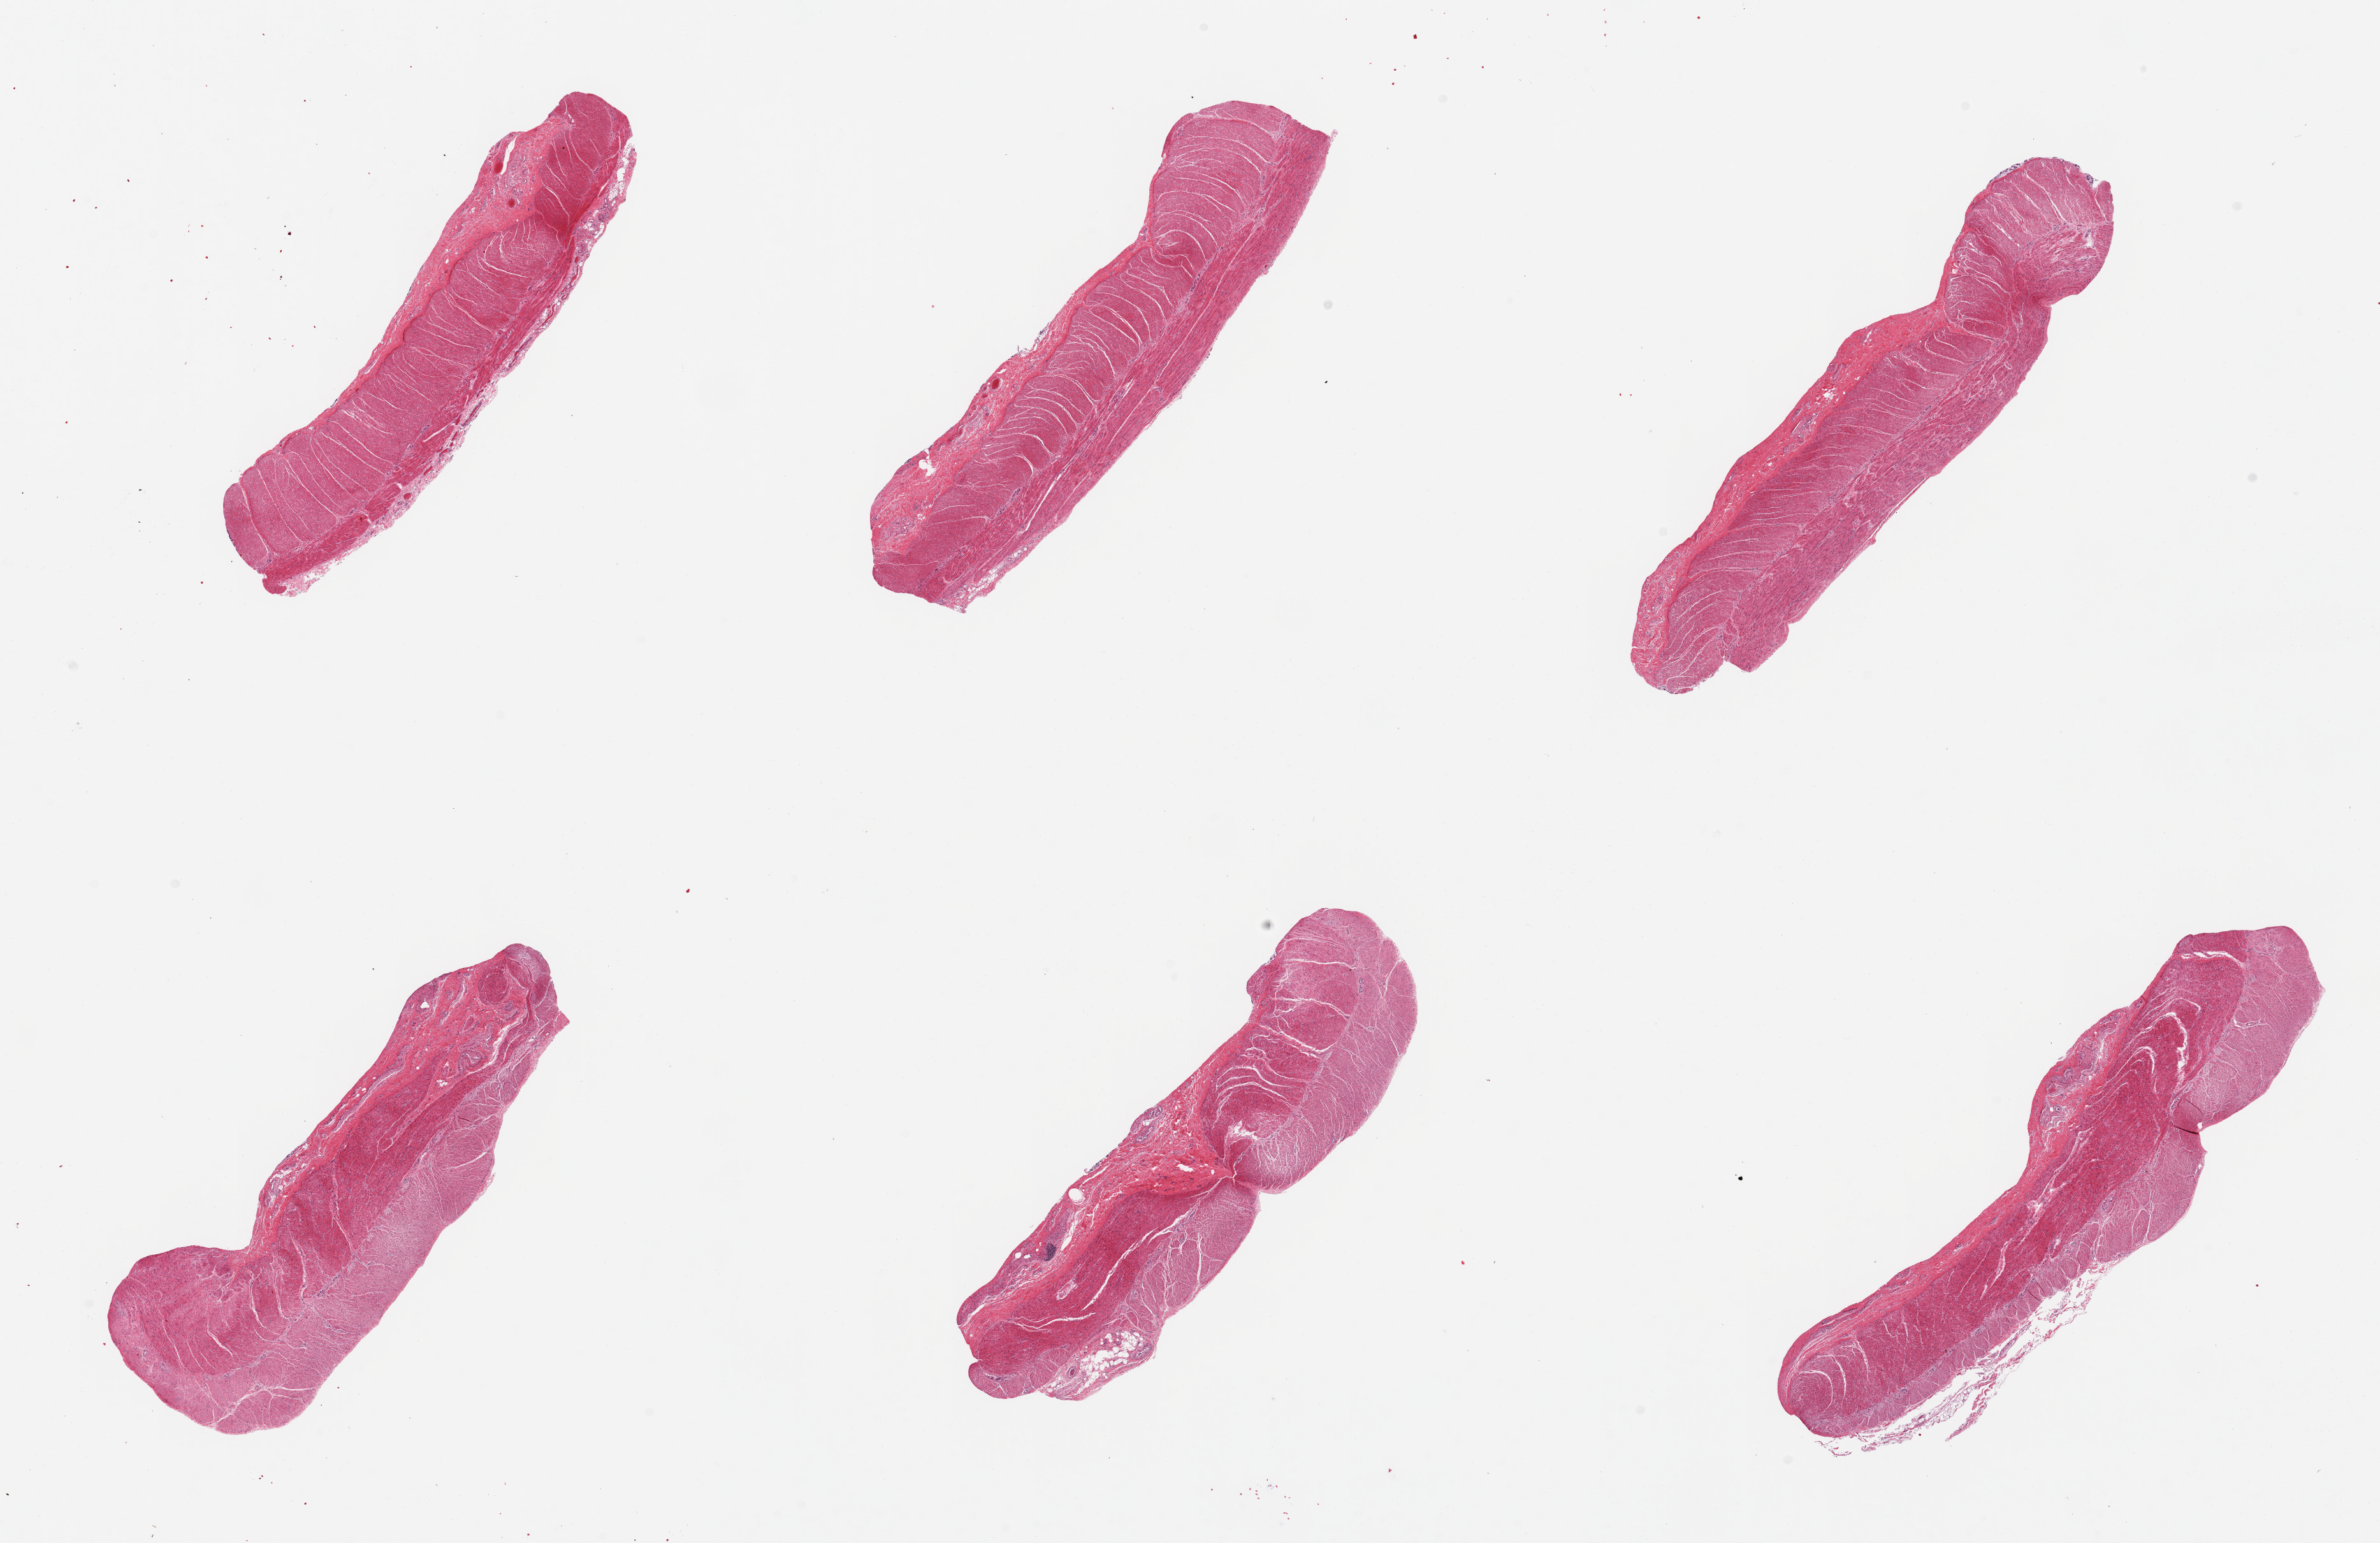
Whole-slide image, H&E stain — shown as a low-resolution overview of the whole scanned area (about 29.5 x 19.1 mm); PAXgene-fixed, paraffin-embedded tissue; sampled site (target tissue): sigmoid colon; donor tissue sample. Donor: female.
Reviewer comment on this tissue sample: 6 pieces, all muscularis.